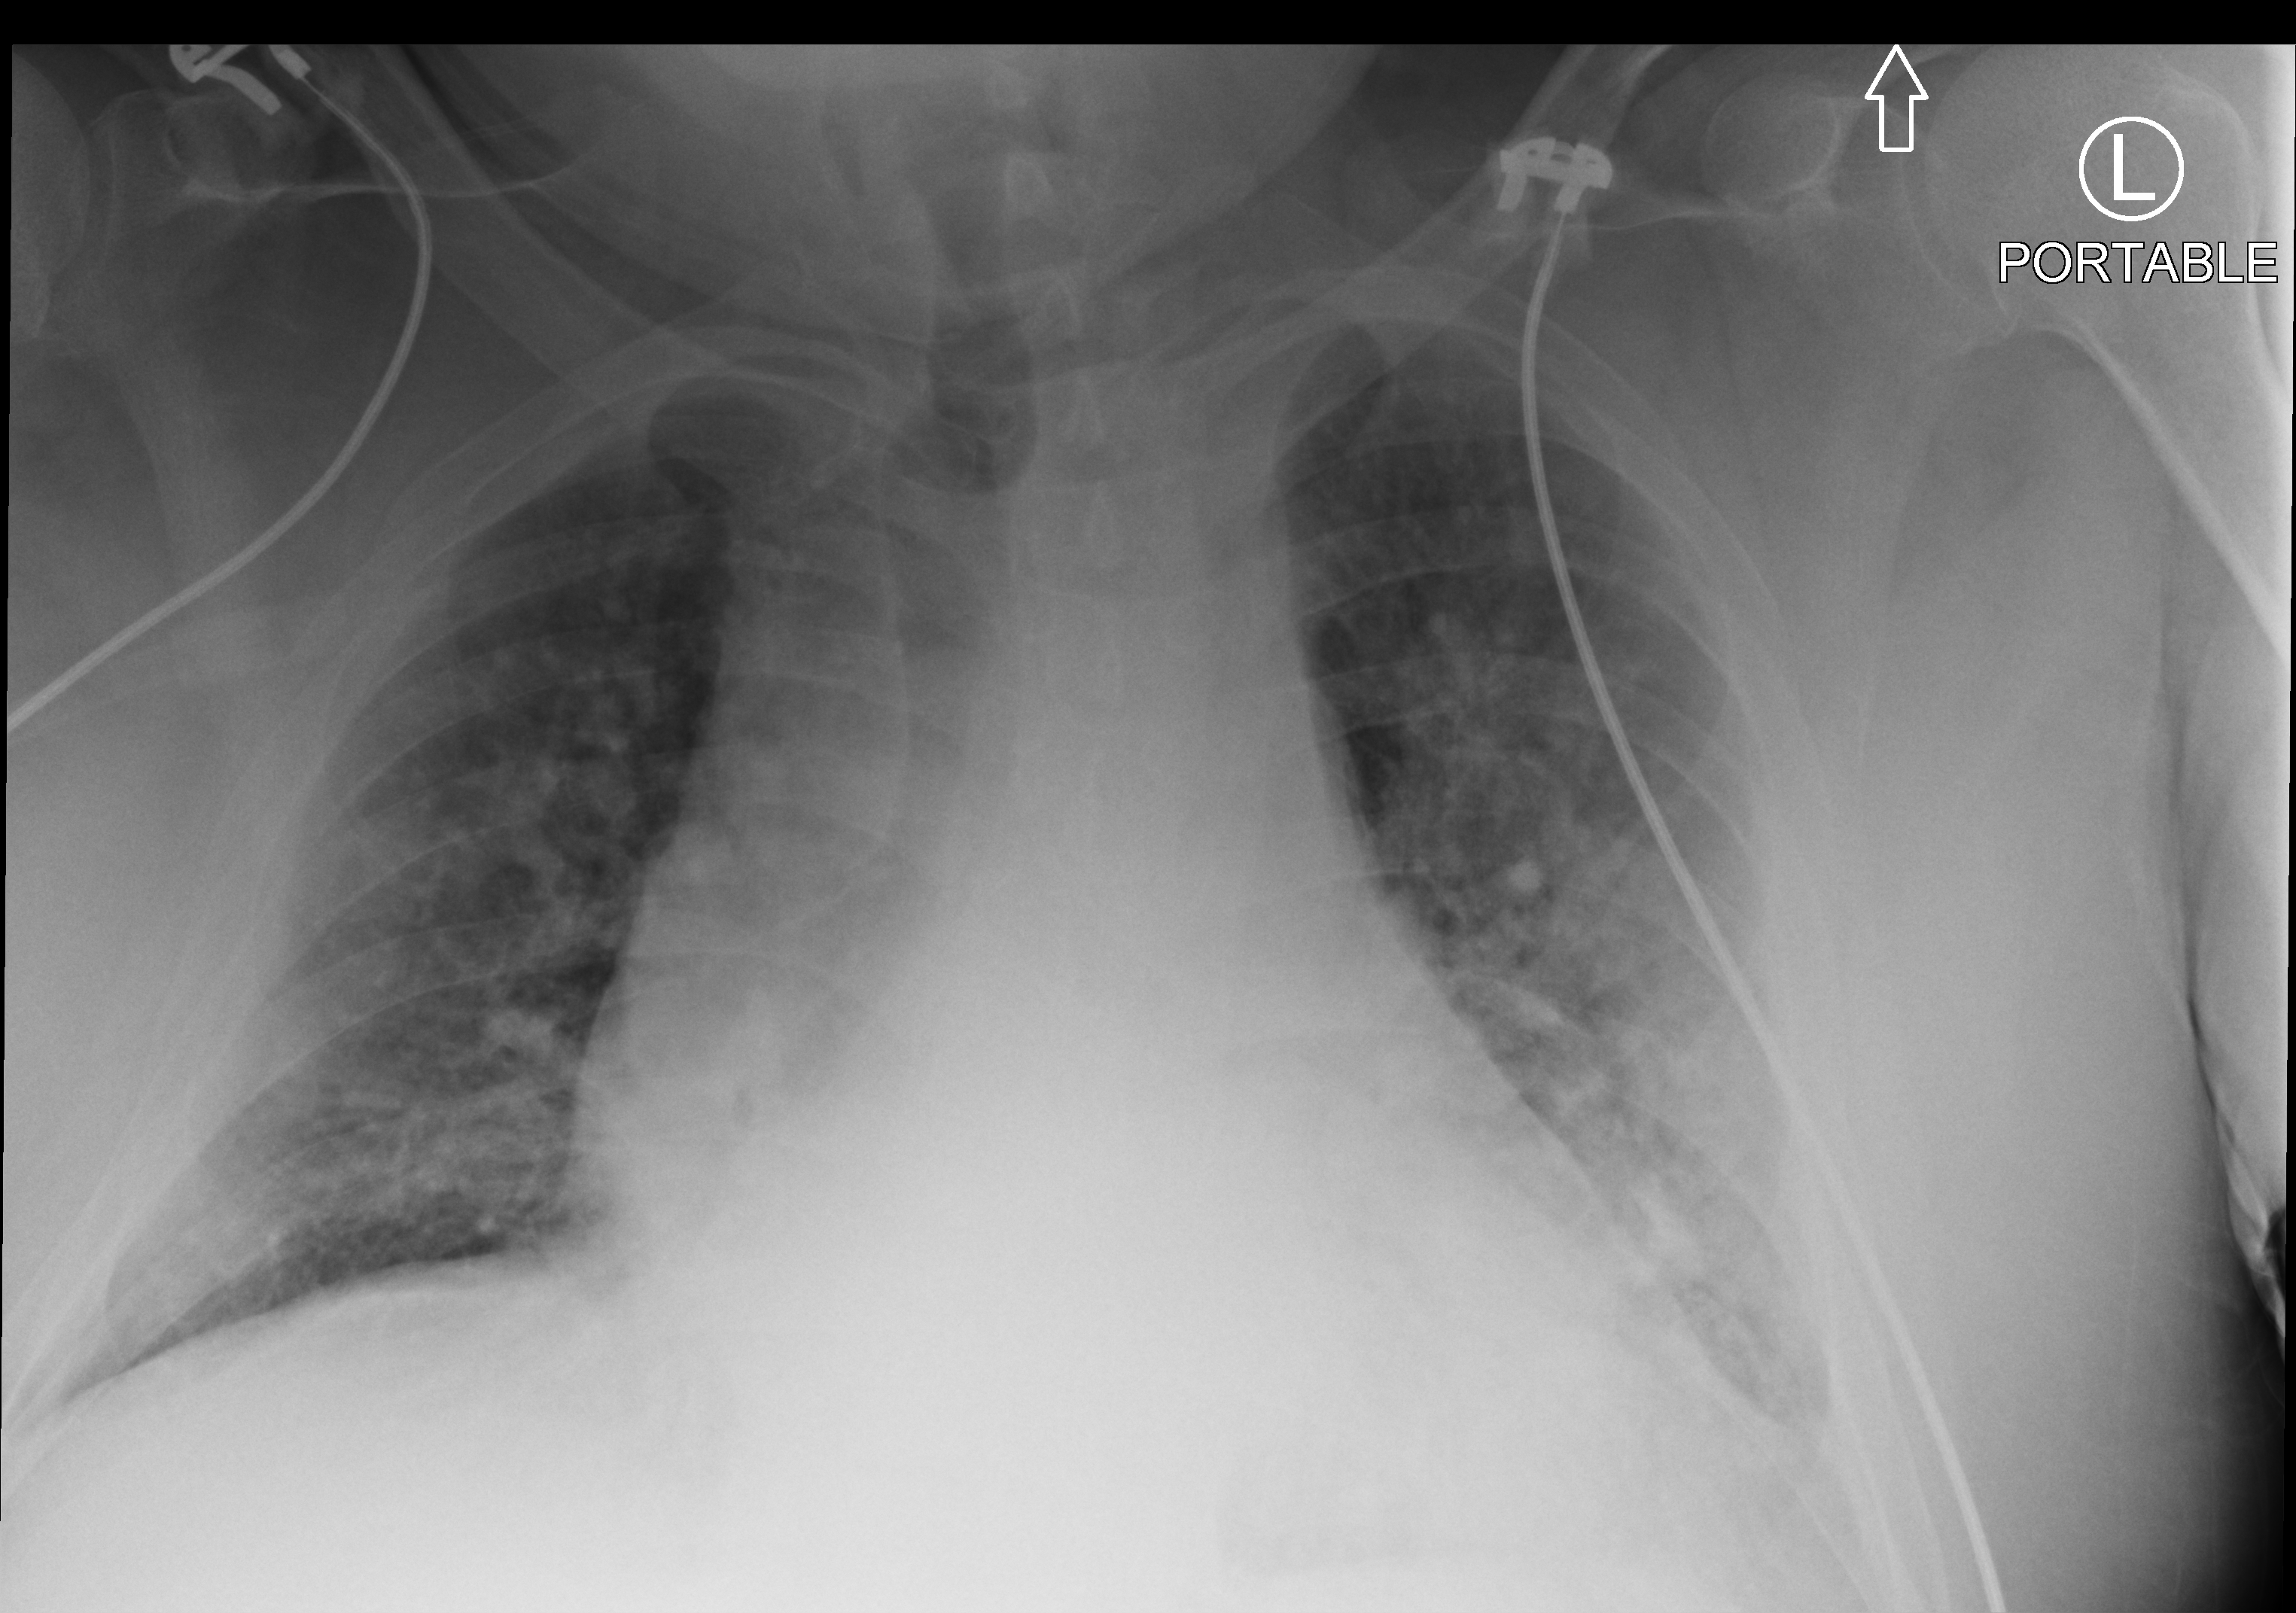
Portable chest radiograph, anteroposterior (AP) projection. Patient hospitalised with COVID-19; male, aged 18–59 years.
Admission-level facts for this patient (not findings on this image; timing relative to this image not recorded): chronic kidney disease (admission record): yes; mechanically ventilated during this hospital stay: no; admitted to intensive care during this hospital stay: no.